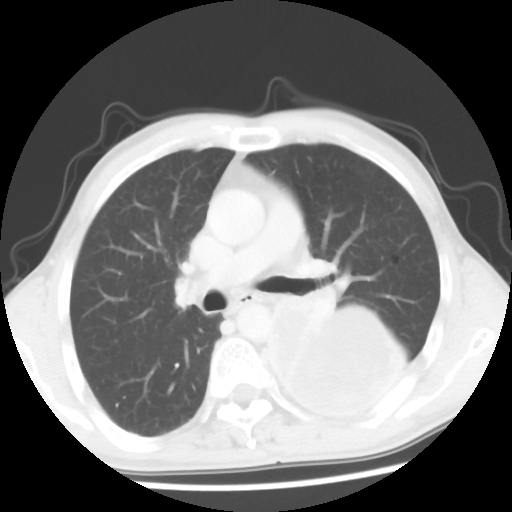
Chest CT, one axial slice; position 34 of 56 along the scan axis; reconstruction kernel STANDARD; 120 kVp; lung window (W 1500 / L -600 HU); 5 mm slice thickness; 512 × 512 image matrix, field of view 318 × 318 mm. Male patient, age 60 years. Case-level facts recorded for this patient, not image findings: clinical TNM (as recorded): T4 N0 M0.
Structures marked on this image (rectangle marked by the reading radiologist):
- lung tumour (recorded histology: squamous cell carcinoma): bounding box [x1, y1, x2, y2] px = [266, 301, 421, 431]